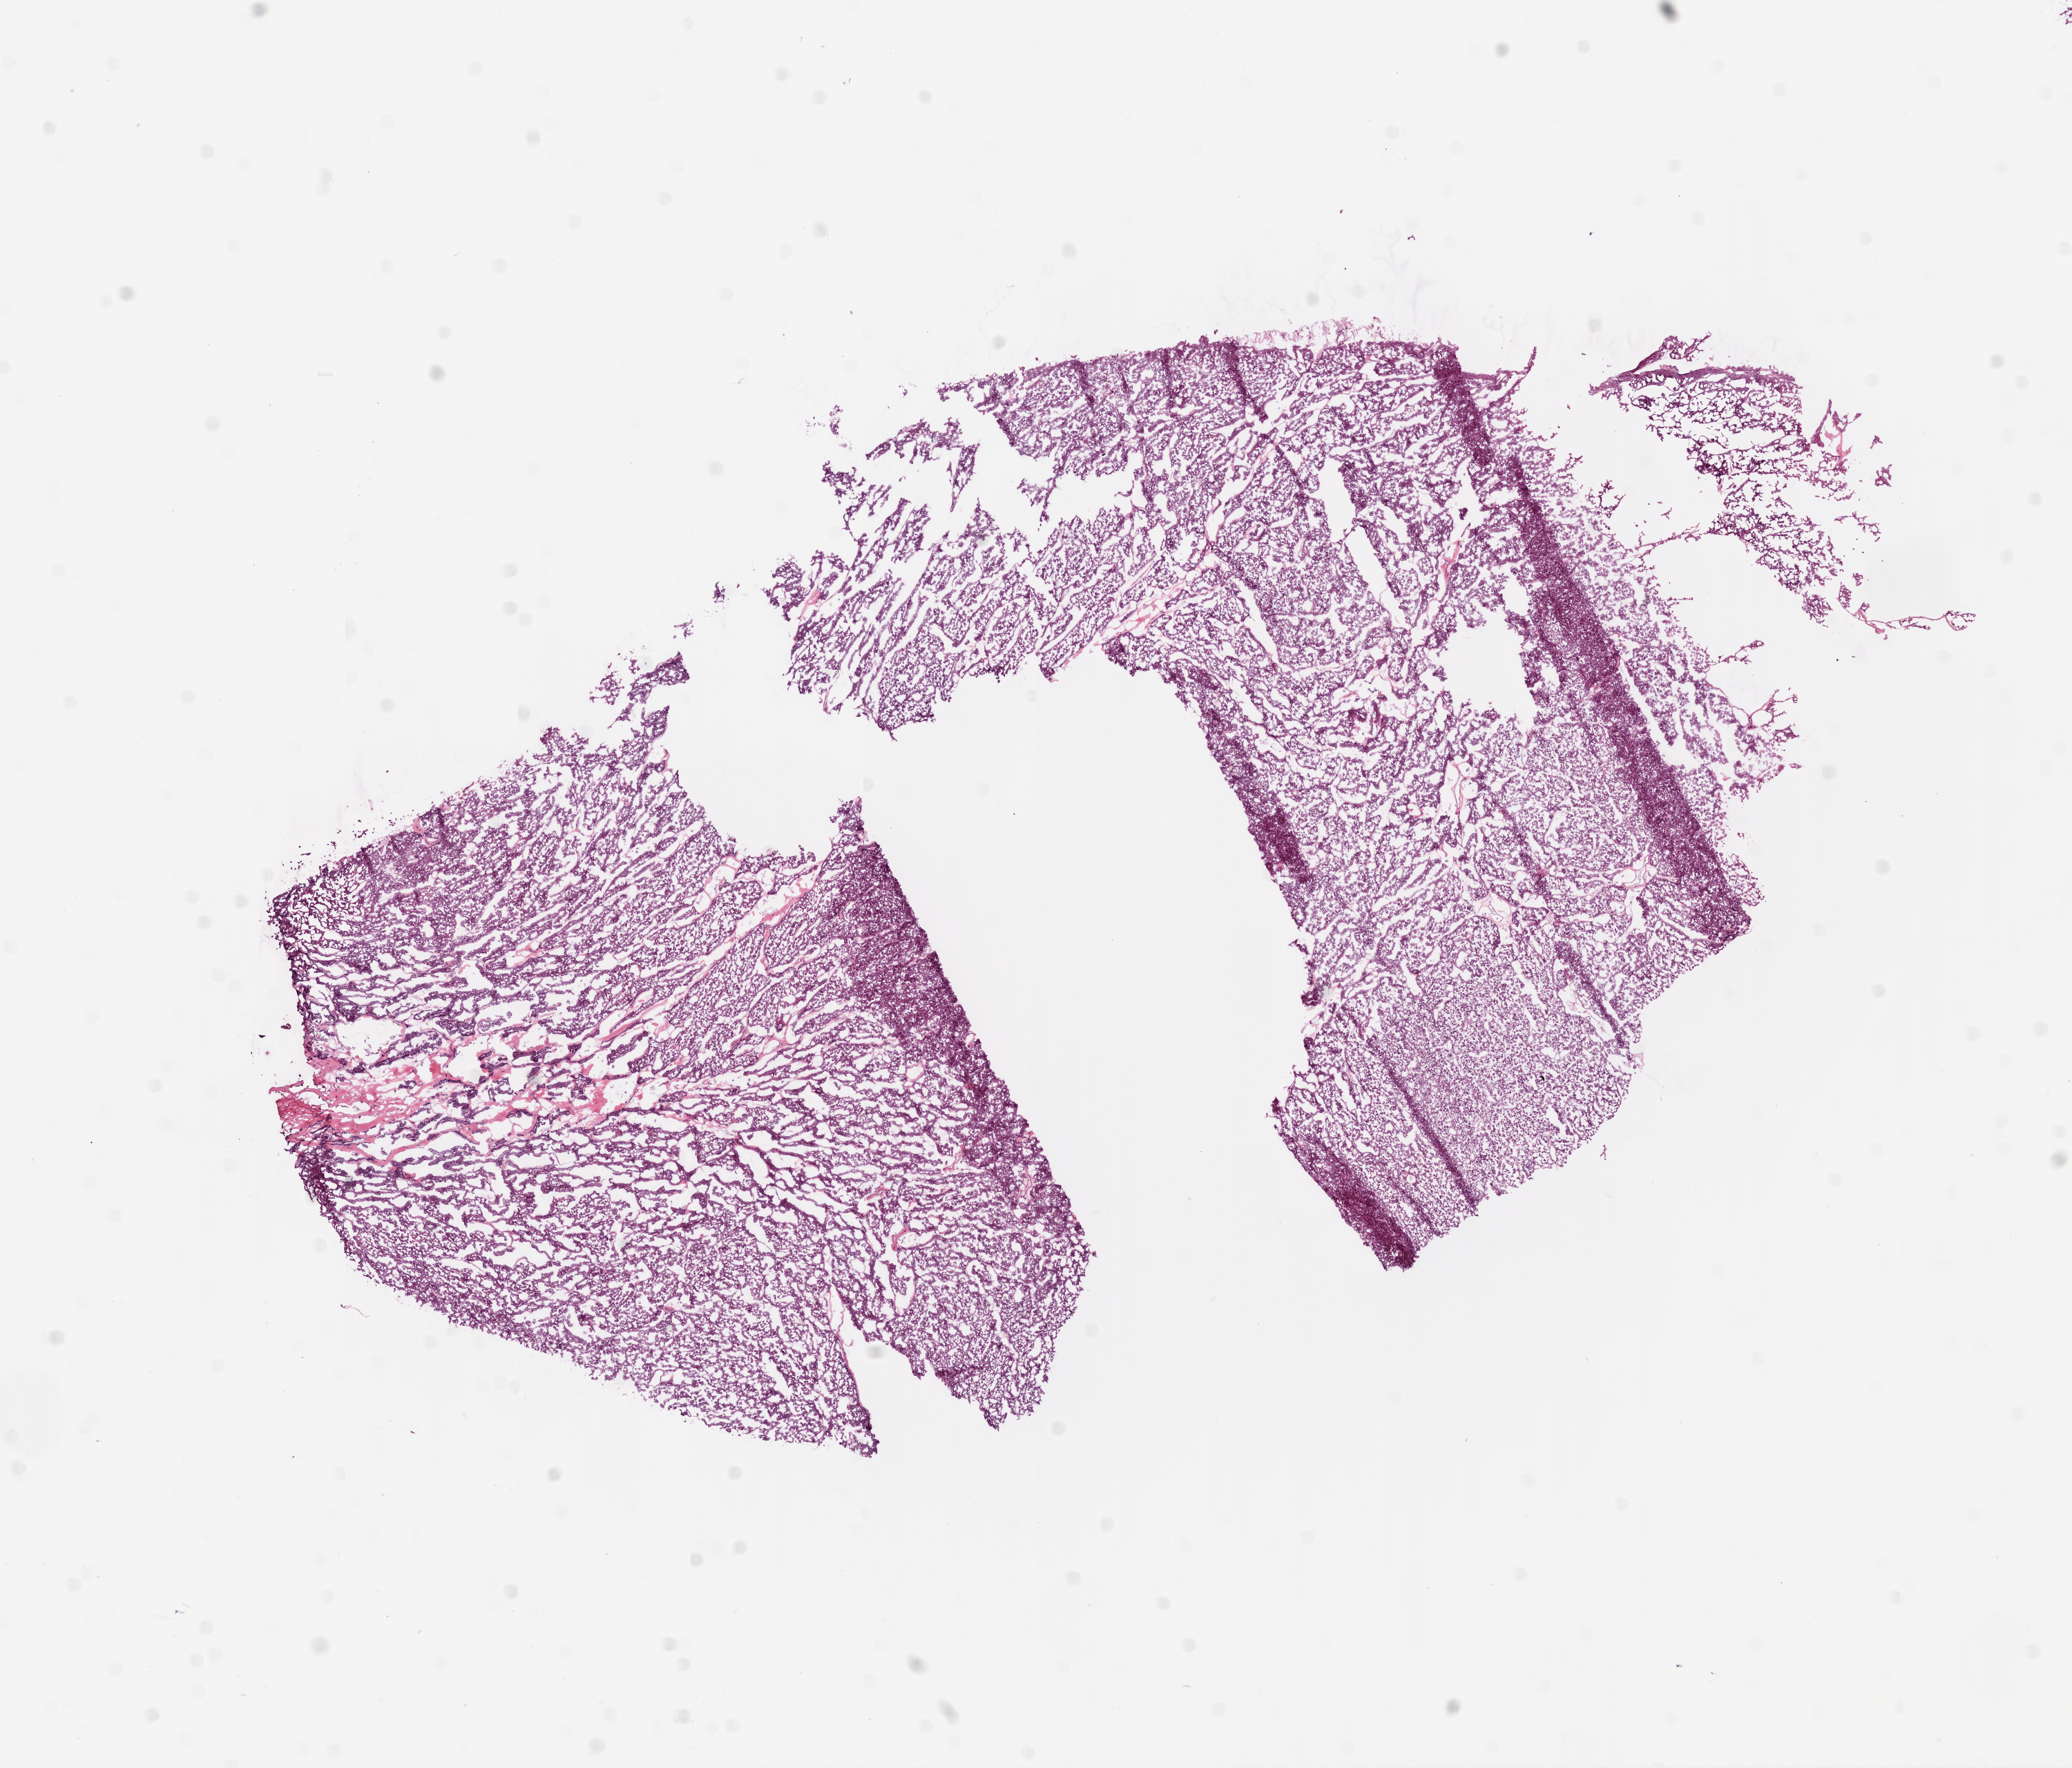
Digitized Hematoxylin and eosin (H&E) stained tissue section (whole slide), low-resolution overview of the scanned area, about 12.0 x 10.3 mm; frozen section; kidney, primary tumour sample. Patient: female, age at initial diagnosis 48 years. Histologic grade: GX (grade cannot be assessed). Composition of this section per pathologist review: tumour cells 90%, tumour nuclei 85%, normal cells 0%, stromal cells 10%, necrosis 0%.
Pathologic diagnosis: Clear cell adenocarcinoma, NOS. AJCC pathologic stage: II (6th edition).